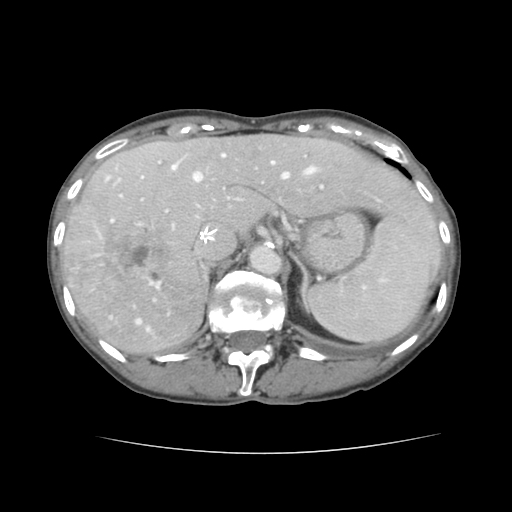
Contrast-enhanced abdominal CT, one axial slice; slice 101 of 136 in the series (ordered by position); intravenous contrast given; soft-tissue window (W 400 / L 40 HU); 2.5 mm slice thickness; 512 × 512 image matrix, field of view 319 × 319 mm. Female patient, age 77 years. Case-level facts recorded for this patient, not image findings: diagnosis: colorectal cancer liver metastases, imaged before liver resection; multiple liver metastases: yes; largest metastasis: 3 cm; disease in both lobes: no.
Annotated regions visible in this slice (outlined manually by an expert reader):
- hepatic veins: bounding box <107,154,316,331> (left, top, right, bottom; pixels)
- liver: <64,134,440,355>
- planned liver remnant (the part of the liver to remain after resection): <158,135,440,261>
- portal vein (with intrahepatic branches): <111,173,382,288>
- liver metastasis: <102,225,177,297>